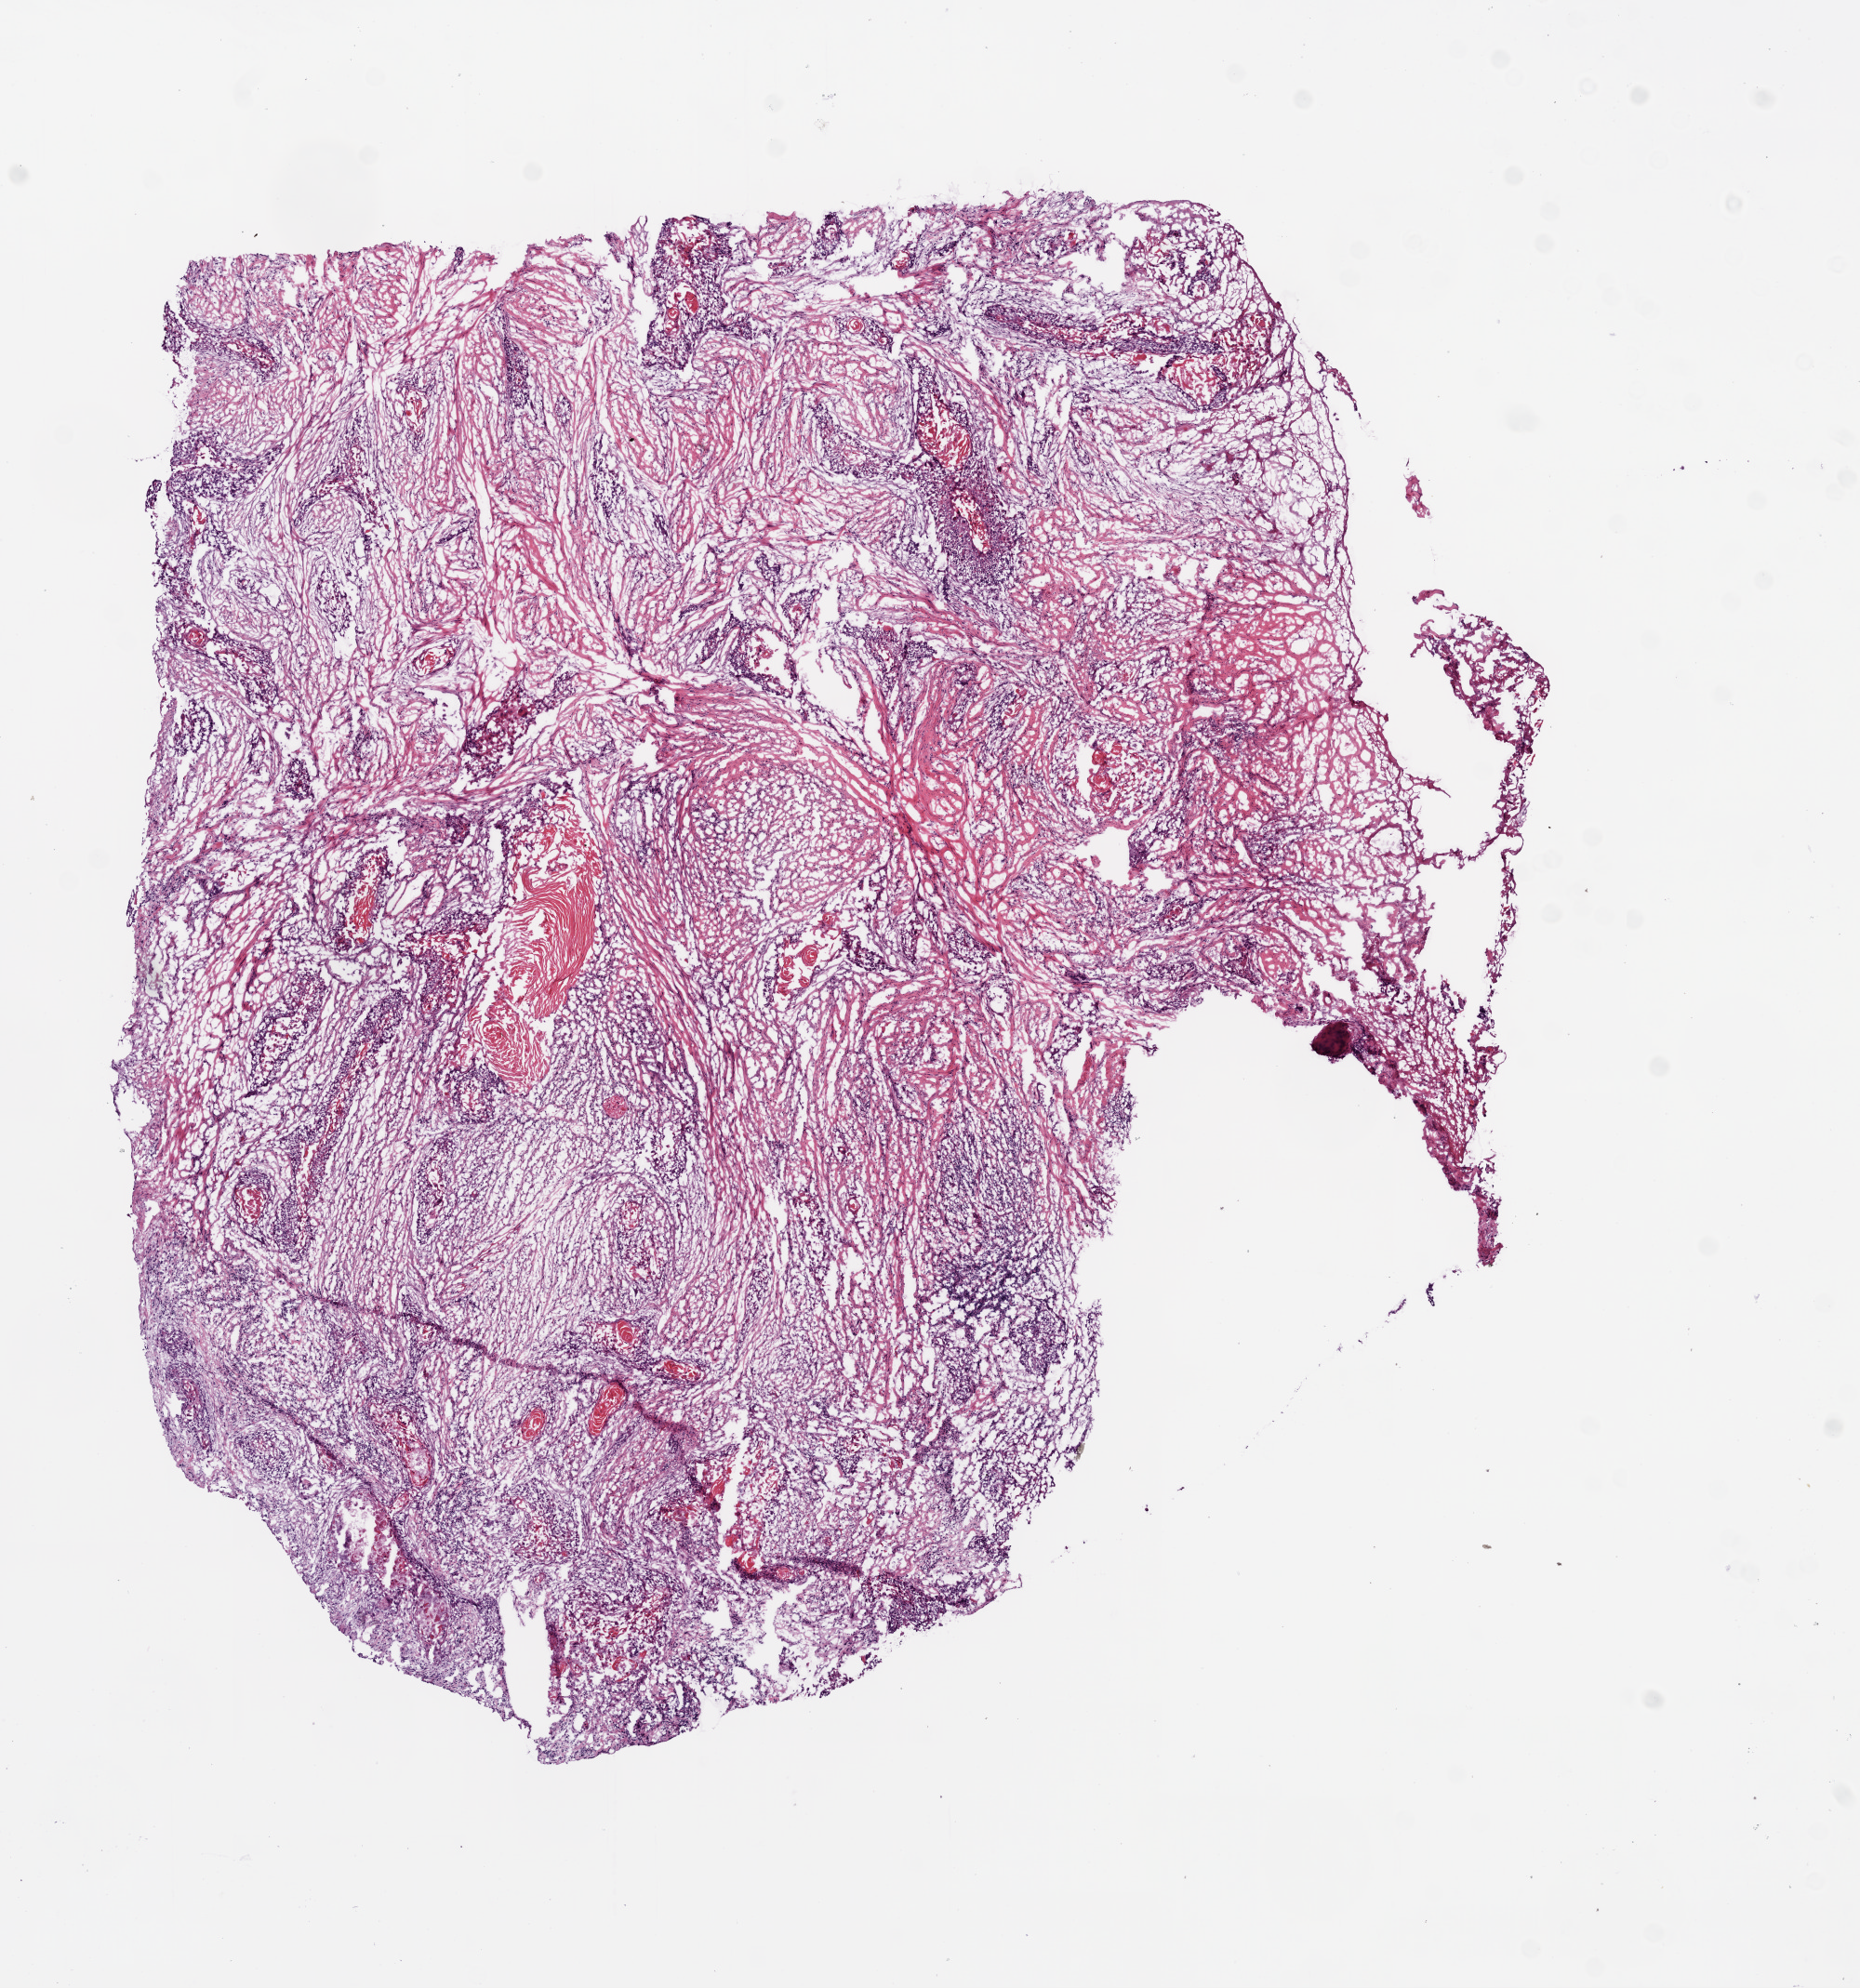
Whole-slide histology image, H&E-stained — a low-resolution overview of the entire scanned area, about 8.0 x 8.6 mm; frozen section from the bottom of the tissue portion; sample: primary tumour, head and neck. Patient: male, age at initial diagnosis 56 years. Histologic grade: G2 (moderately differentiated). Pathologist review of this section (percent, as recorded): tumour cells 45%, tumour nuclei 65%, normal cells 0%, stromal cells 50%, necrosis 5%.
- AJCC pathologic stage: IVA
- histologic diagnosis: Squamous cell carcinoma, NOS (overlapping lesion of lip, oral cavity and pharynx)